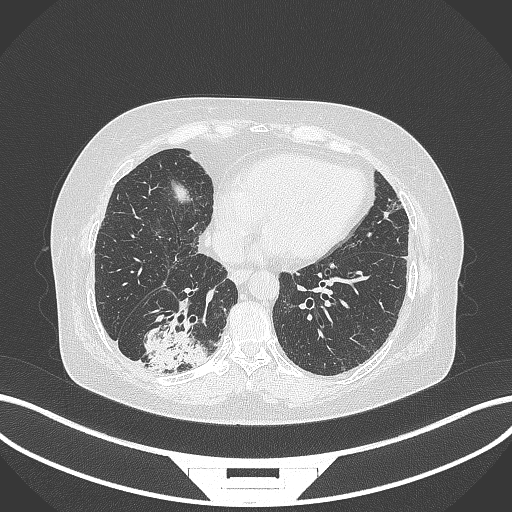
Chest CT, one axial slice; slice 73 of 296 in the series (ordered by position); lung window (W 1500 / L -600 HU); 1 mm slice thickness; 512 × 512 image matrix, field of view 400 × 400 mm. Female patient, age 65 years. Case-level facts recorded for this patient, not image findings: clinical TNM (as recorded): T2b N1 M0.
Structures marked on this image (bounding box drawn by a radiologist):
- lung tumour (recorded histology: adenocarcinoma): bounding box [x1, y1, x2, y2] px = [142, 319, 210, 374]